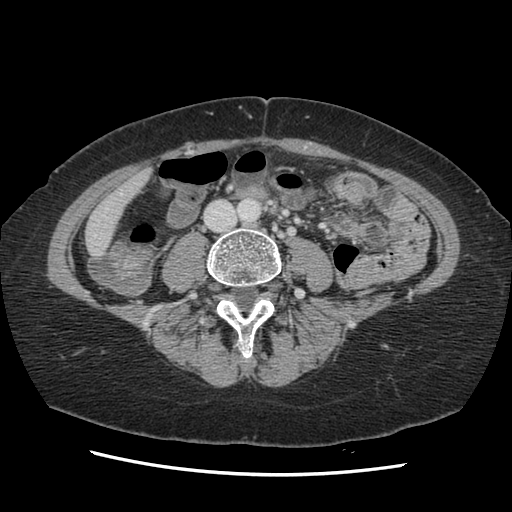
Contrast-enhanced abdominal CT, one axial slice; position 18 of 141 along the scan axis; soft-tissue window (W 400 / L 40 HU); 512 × 512 image matrix, field of view 330 × 330 mm. Female patient, age 61 years. From the clinical record (not read from this slice): diagnosis: colorectal cancer liver metastases, imaged before liver resection; multiple liver metastases: no; largest metastasis: 2.4 cm; chemotherapy before resection: no.
Annotated regions visible in this slice (expert manual segmentation):
- liver: box from (x=87, y=172) to (x=149, y=254) px
- planned liver remnant (the part of the liver to remain after resection): (x=87, y=172)–(x=149, y=254)